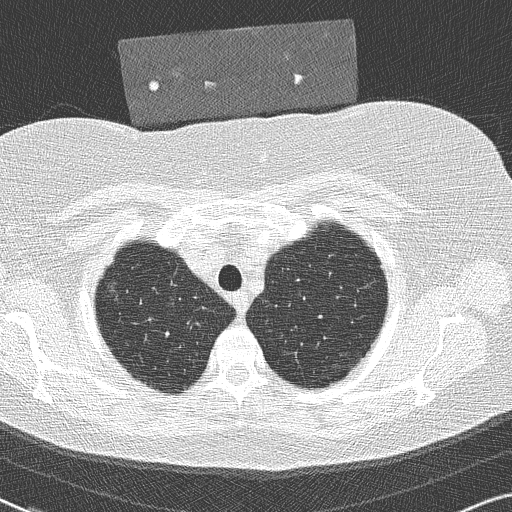
Axial slice from a low-dose chest CT screening exam. Baseline screening round. Lung window (W 1500 / L -600 HU). 2 mm slice thickness. Lung (sharp) reconstruction kernel (B50f). 120 kVp. 512 × 512 image matrix. Female participant, aged 58 years at enrolment. Former smoker at enrolment.
Expert reader's lesion annotation, bounding box <95,251,131,298> (left, top, right, bottom; pixels). Screening reader's record for this exam: no non-calcified nodule ≥4 mm recorded. Official screen result: negative screen, minor abnormalities not suspicious for lung cancer. Participant outcome: lung cancer diagnosed 846 days after this screen — bronchiolo-alveolar adenocarcinoma, NOS, right upper lobe, well differentiated (G1), stage IA (AJCC 6th edition), 9 mm at pathology.